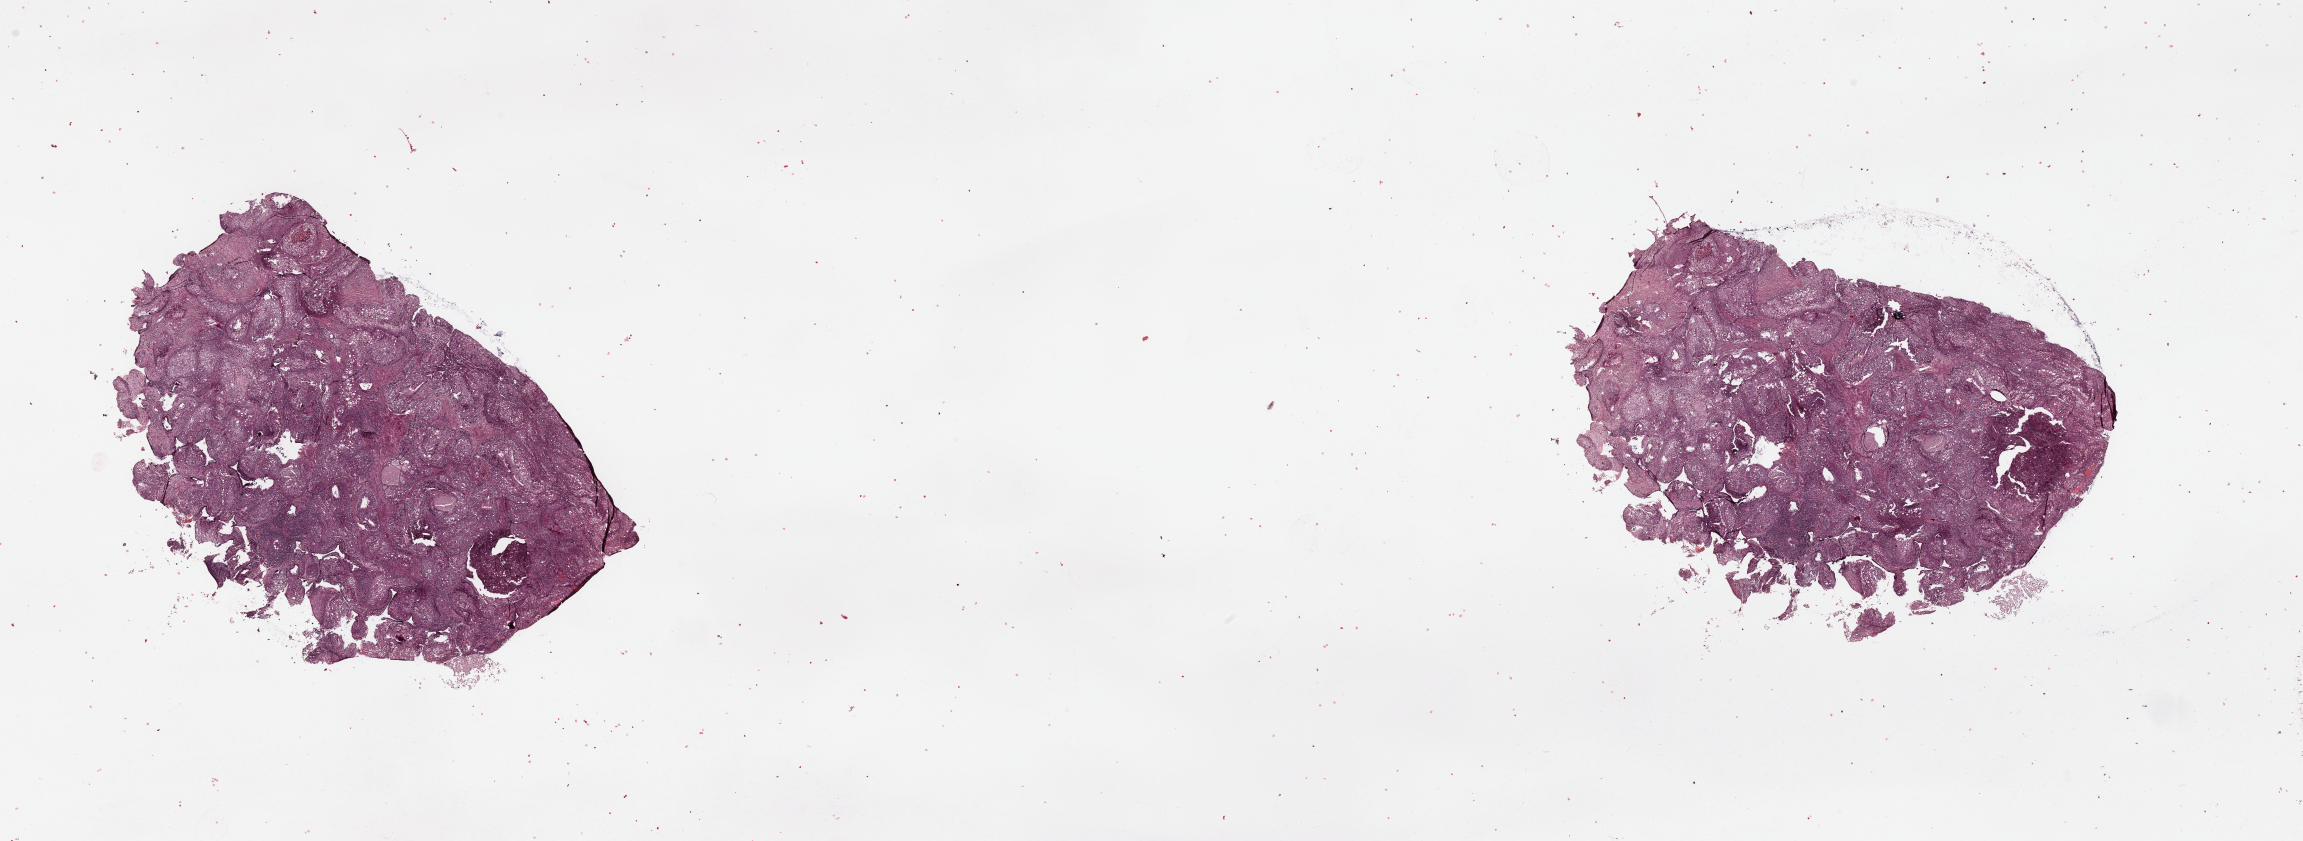
H&E-stained whole-slide image, shown as a low-resolution overview of the whole scanned area (about 36.4 x 13.3 mm, slide scanned at 20x). Tumour tissue sample, lung. Patient: male, age 68 years.
Patient diagnosis (cohort enrolment): squamous cell carcinoma (lung).